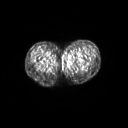
FDG PET of an extremity soft-tissue mass (from a PET/CT study), one axial slice; position 36 of 267 along the scan axis; 3.27 mm slice thickness; 128 × 128 image matrix. Patient: female, 24 years. Case-level facts recorded for this patient, not image findings: histological type: leiomyosarcoma; grade: high; site of the primary tumour: groin.
Annotated regions visible in this slice (expert contour drawn on MRI and transferred to this co-registered scan by the dataset authors):
- gross tumour volume including surrounding oedema: bounding box <62,55,69,63> (left, top, right, bottom; pixels)